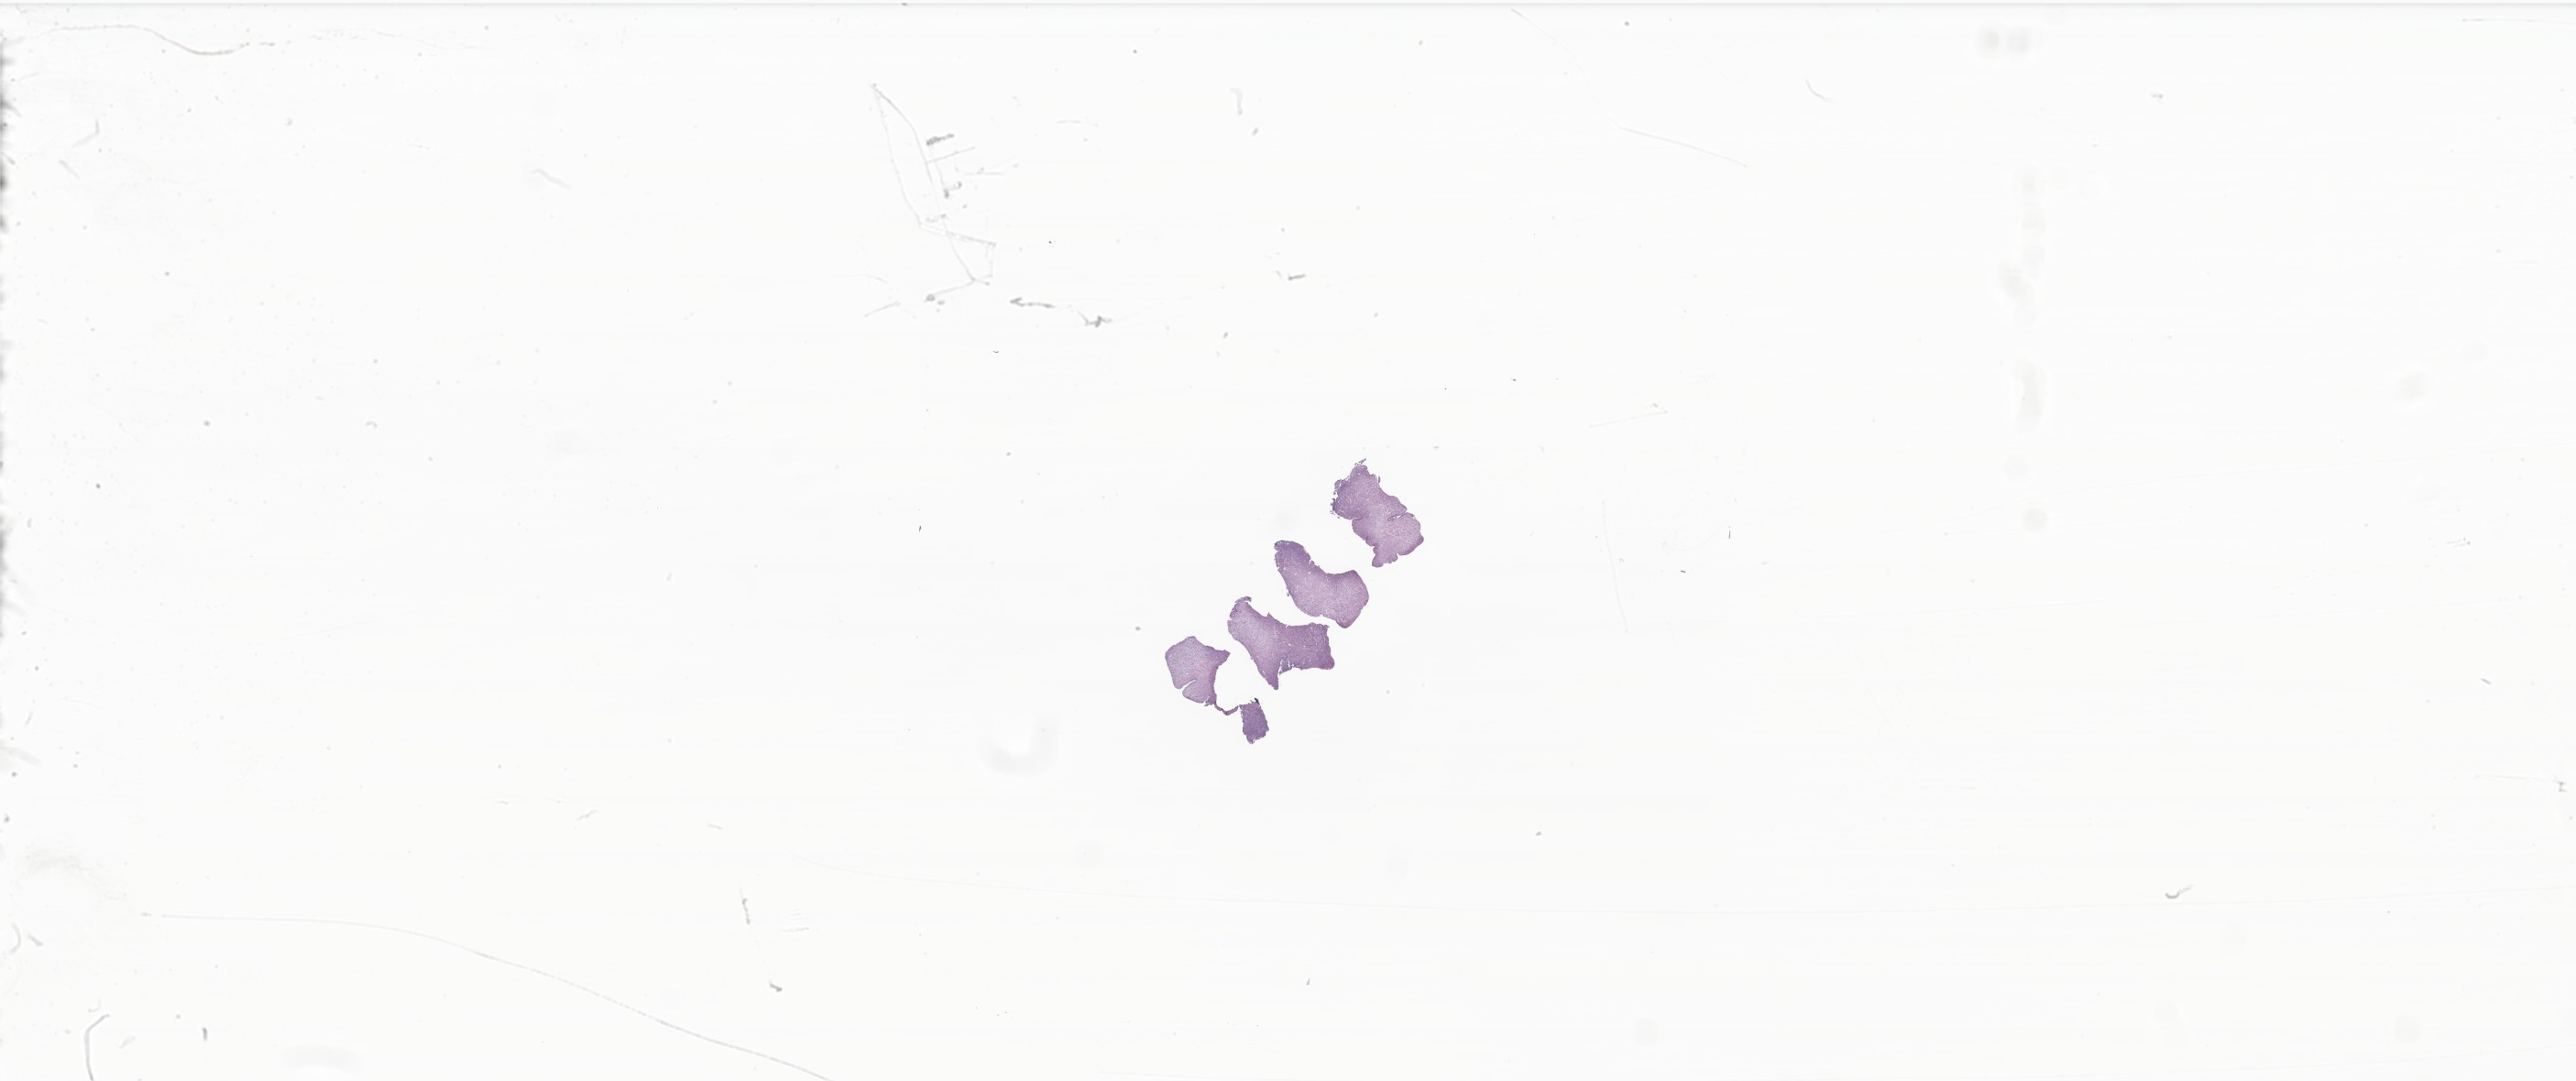
Digitized haematoxylin and eosin-stained section of tumor tissue from the urinary bladder — whole scanned area (about 47.4 x 19.9 mm) shown as a low-resolution overview. Formalin-fixed paraffin-embedded section. Male patient, age 59 days.
Recorded diagnosis: Embryonal rhabdomyosarcoma, NOS.